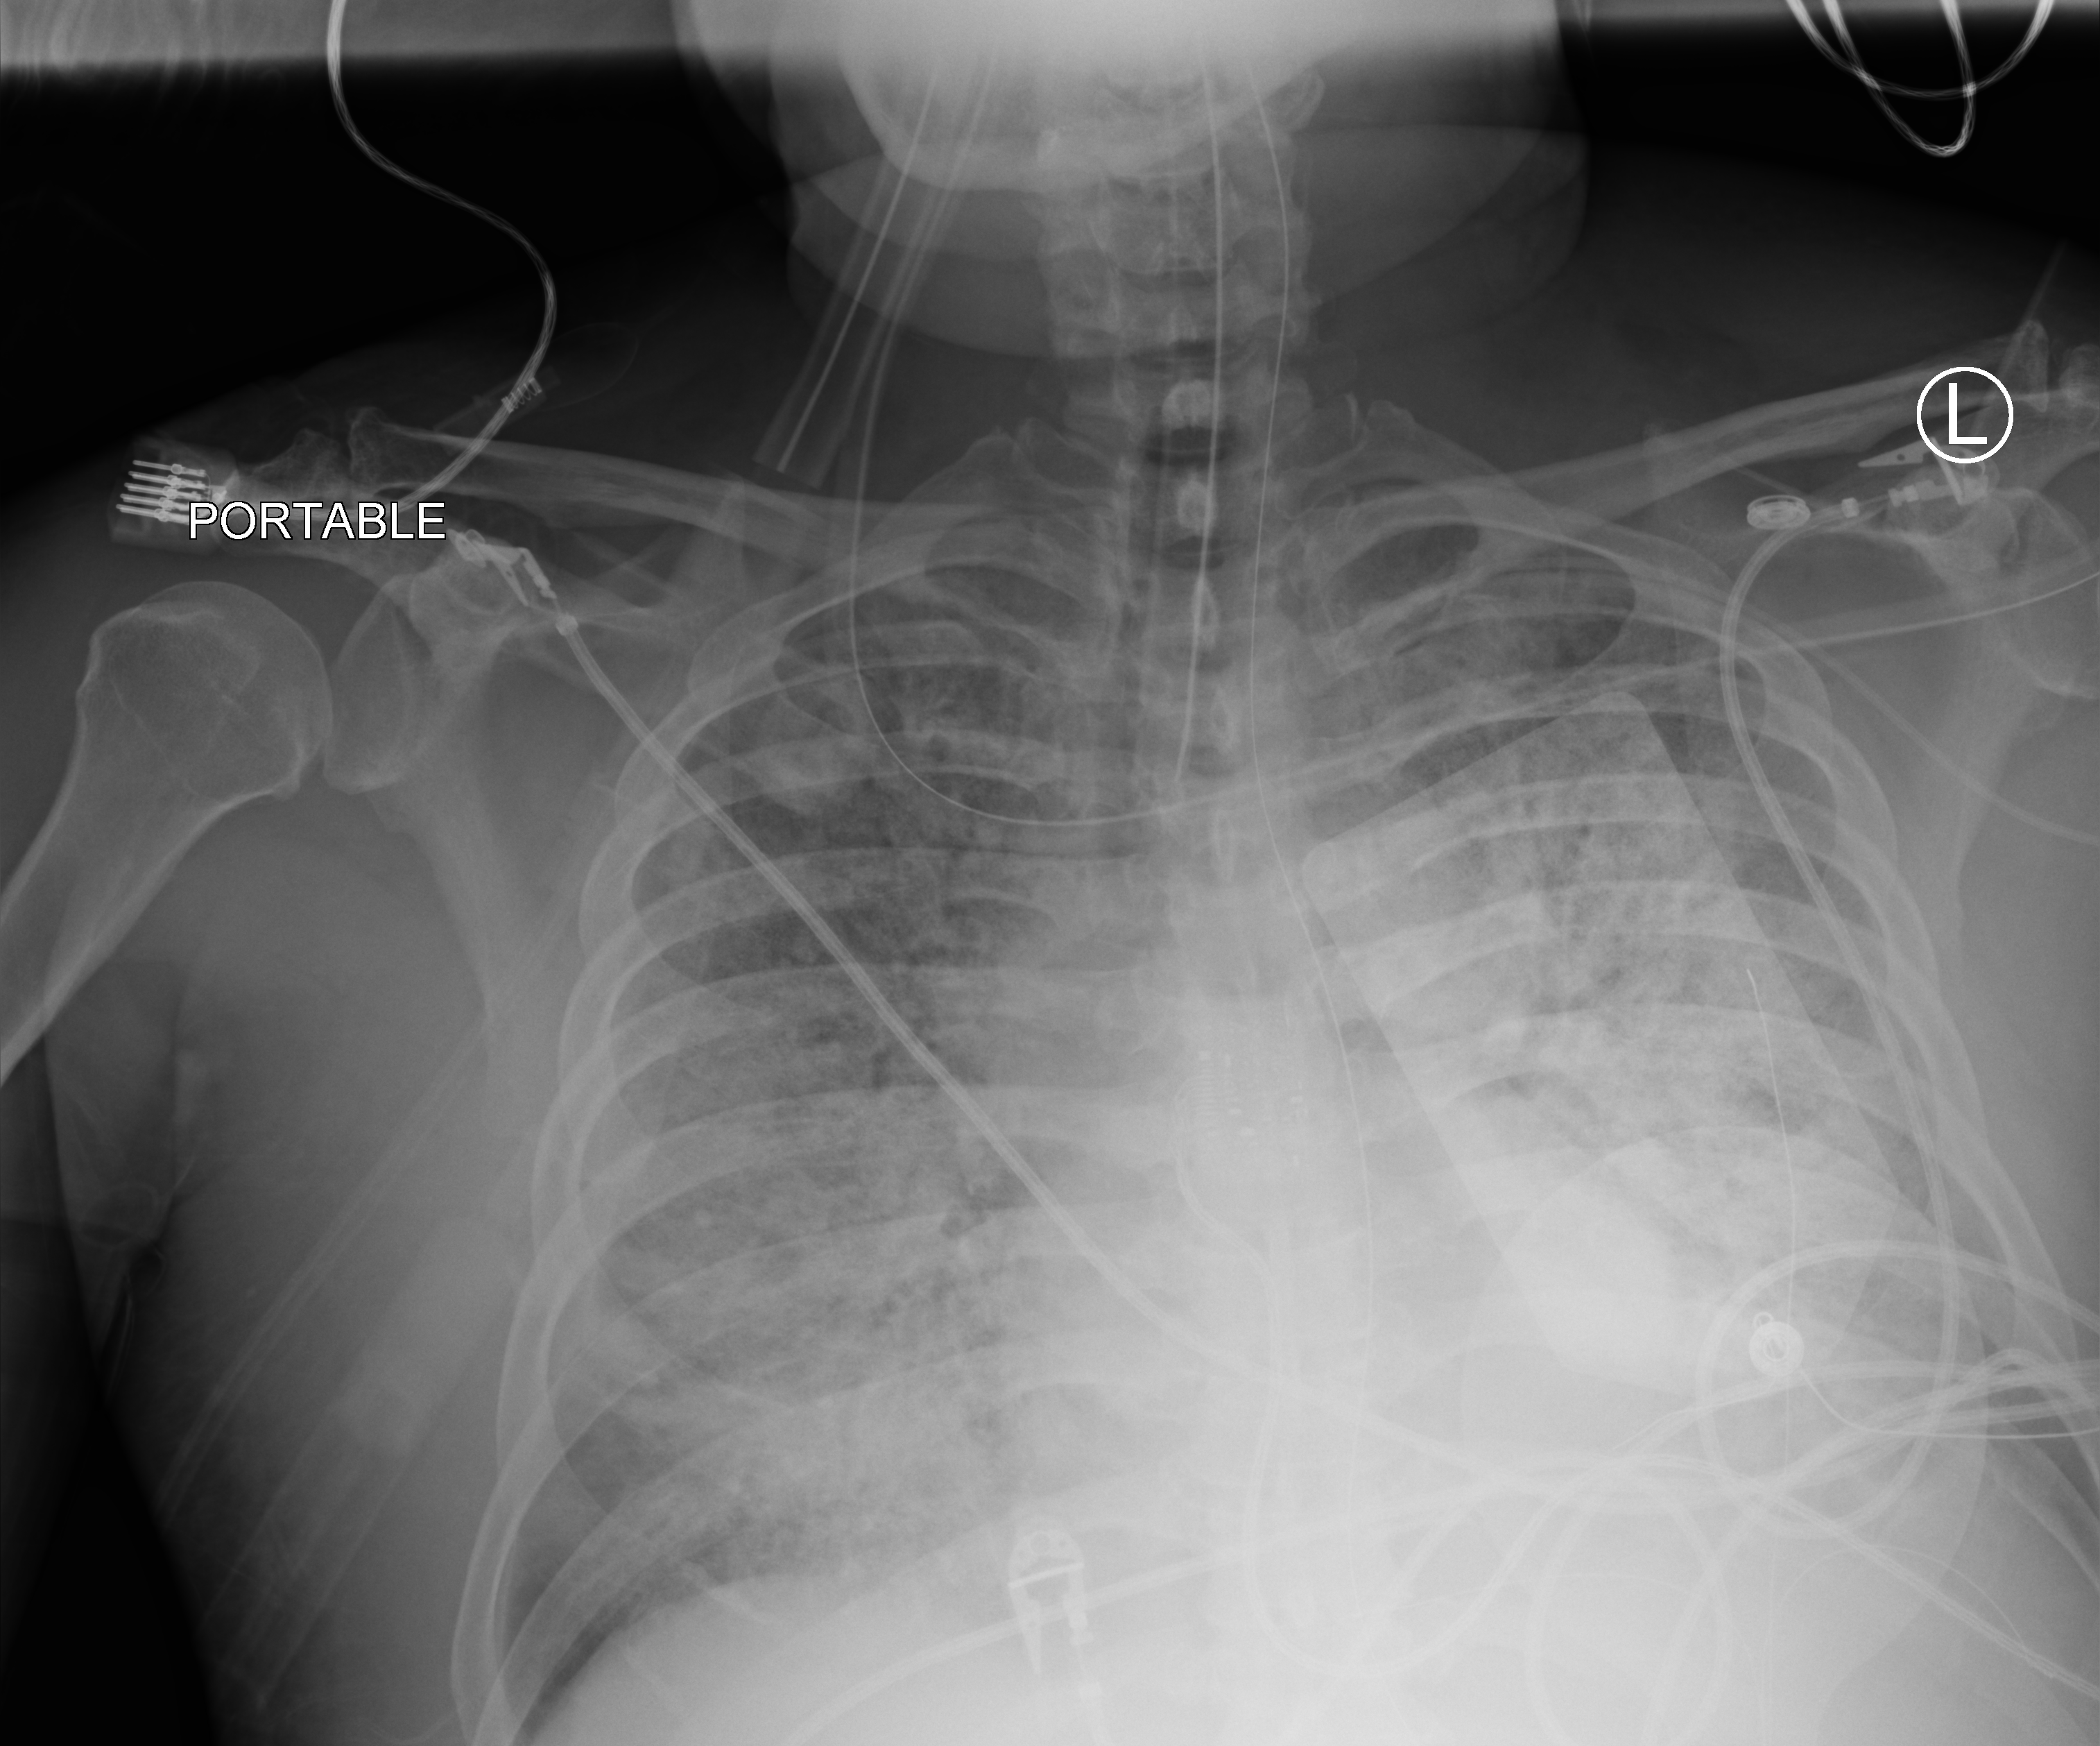
Chest X-ray (portable), anteroposterior (AP) projection. Male patient hospitalised with COVID-19, age 60–74 years.
From the hospital-stay record, not from the radiograph (when in the stay this image was taken is not recorded): admitted to intensive care during this hospital stay: yes.